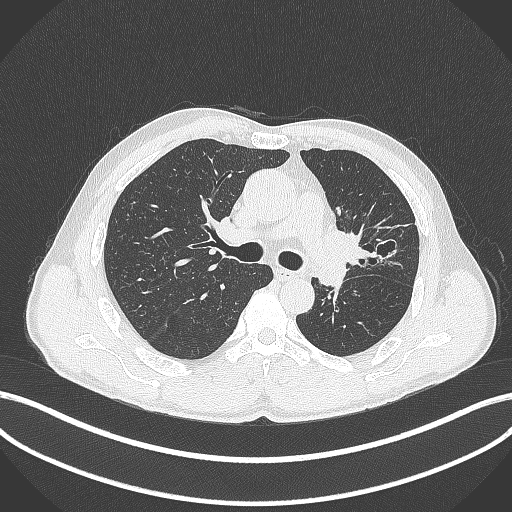
Chest CT, one axial slice; slice 264 of 429 in the series (ordered by position); 120 kVp; lung window (W 1500 / L -600 HU); 1 mm slice thickness; 512 × 512 image matrix. Male patient, age 57 years. From the clinical record (not read from this slice): clinical TNM (as recorded): T2b N0 M0.
Structures marked on this image (bounding box drawn by a radiologist):
- lung tumour (recorded histology: squamous cell carcinoma): box from (x=321, y=222) to (x=381, y=269) px